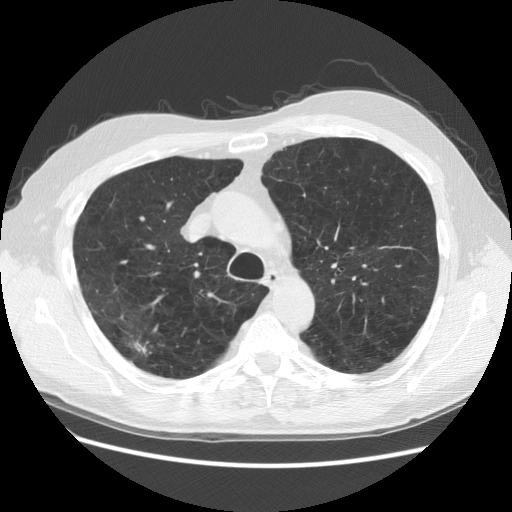
Low-dose screening chest CT, one axial slice; position 97 of 137 along the scan axis; 140 kVp; lung window (W 1500 / L -600 HU); 2.5 mm slice thickness; 512 × 512 image matrix, field of view 377 × 377 mm.
Structures marked on this image (outlined manually by an expert reader):
- lesion 2 (nodule, upper lobe of right lung): bounding box [x1, y1, x2, y2] px = [135, 341, 148, 355]